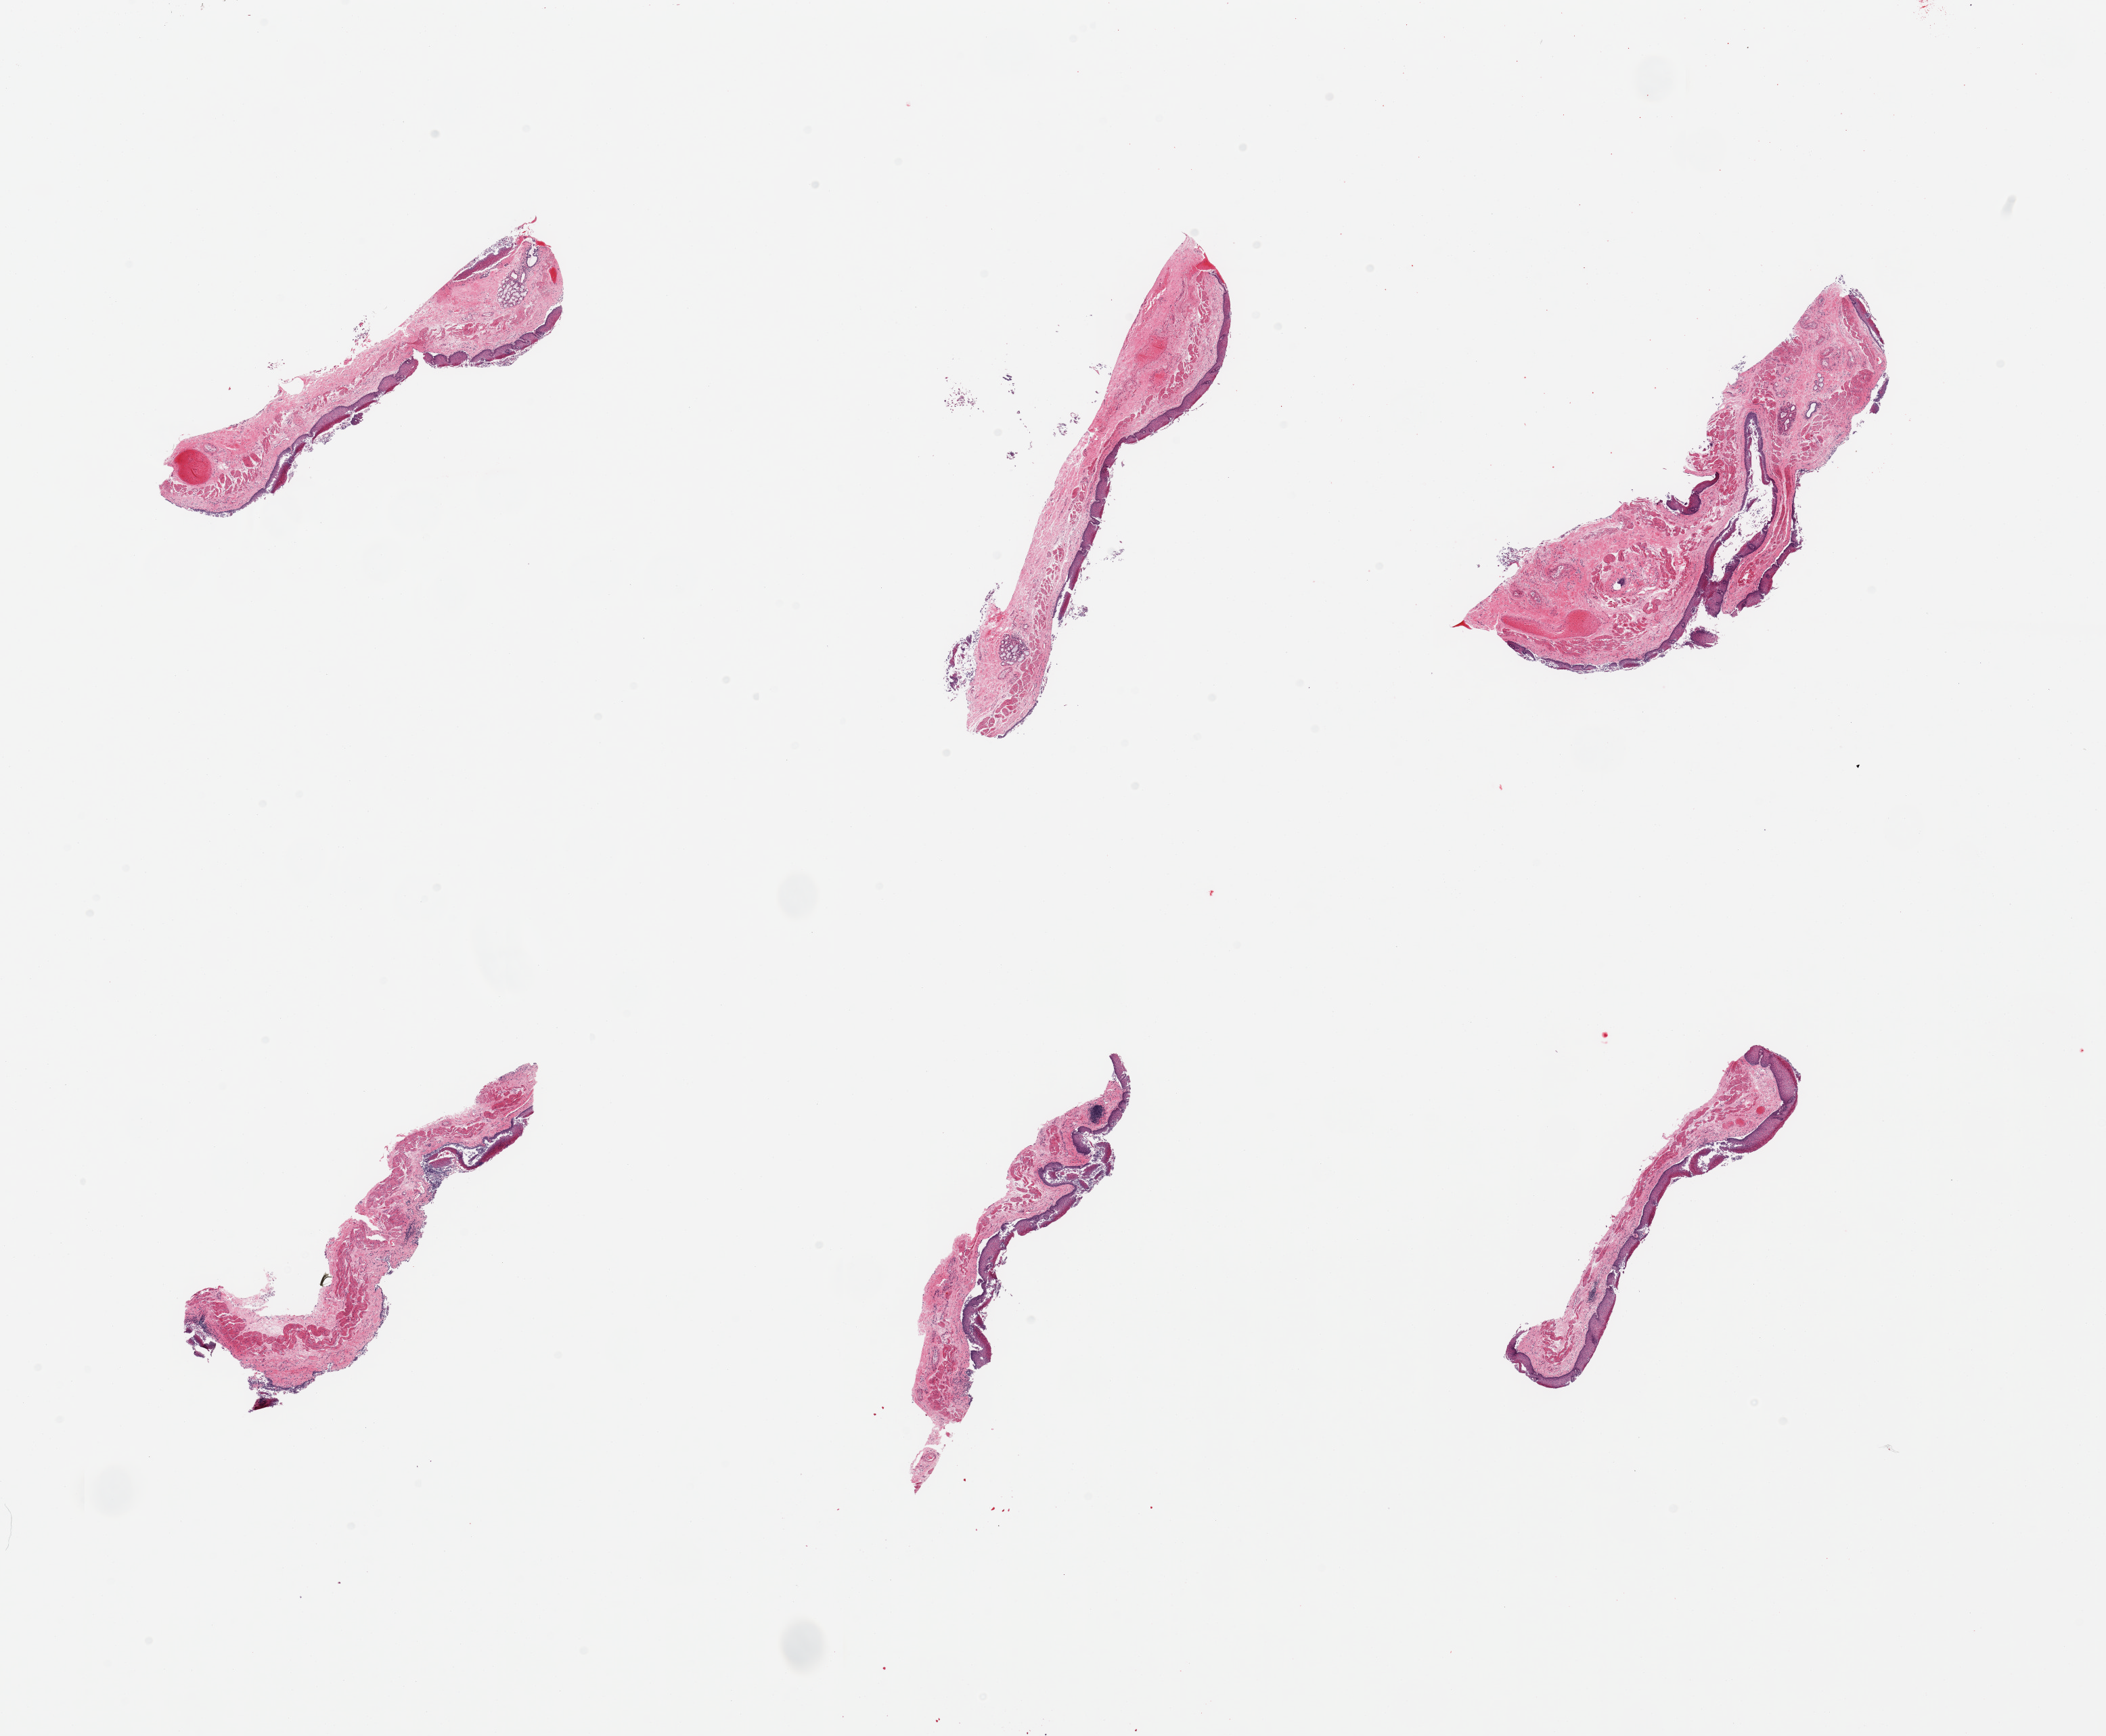
Whole-slide image, H&E stain, shown as a low-resolution overview of the whole scanned area (about 24.6 x 20.3 mm). PAXgene-fixed, paraffin-embedded tissue. Sampled site (target tissue): esophageal mucous membrane. Donor tissue sample. Donor: female.
Pathologist's review note for this sample: 6 pieces squamous mucosa is ~ 150 microns, slouging, unusually poorly preserved.